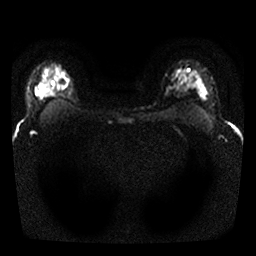
Breast MRI, one axial slice. Position 21 of 25 along the scan axis. Diffusion-weighted series; image 2 of 4 stored at this slice position (different b-values; order by instance number). 1.5 T. 4 mm slice thickness. 256 × 256 image matrix, field of view 300 × 300 mm. Female patient.
Structures marked on this image (outlined manually by an expert reader):
- tumour on diffusion-weighted imaging: bounding box [x1, y1, x2, y2] px = [55, 72, 69, 90]